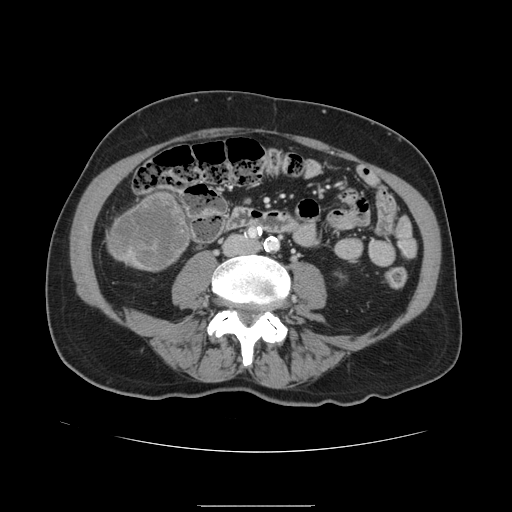
Contrast-enhanced abdominal CT, one axial slice. Position 18 of 168 along the scan axis. 120 kVp. Intravenous contrast given. Soft-tissue window (W 400 / L 40 HU). 2.5 mm slice thickness. 512 × 512 image matrix. Male patient, age 74 years. From the clinical record (not read from this slice): diagnosis: colorectal cancer liver metastases, imaged before liver resection; multiple liver metastases: no; largest metastasis: 14.5 cm.
Annotated regions visible in this slice (outlined manually by an expert reader):
- liver: bounding box <108,189,192,272> (left, top, right, bottom; pixels)
- liver metastasis: <111,195,188,270>